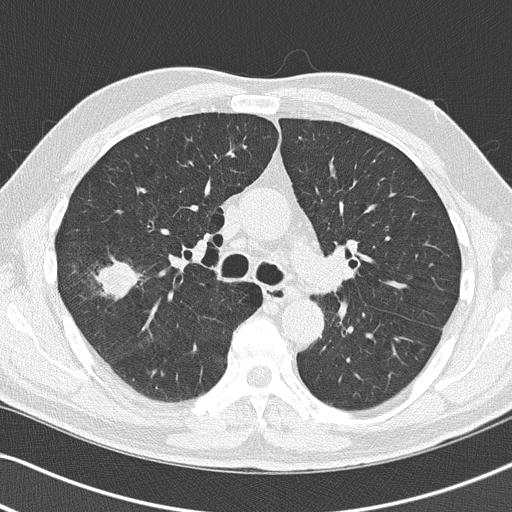
Low-dose screening chest CT, axial slice. First (baseline) screen. Lung window (W 1500 / L -600 HU). 2 mm slice thickness. Male participant, aged 67 years at enrolment.
Expert reader's lesion annotation, bounding box [x1, y1, x2, y2] px = [72, 254, 148, 318]. Screening reader's record for this exam (one nodule recorded; not confirmed to be the boxed lesion): non-calcified nodule or mass ≥4 mm, right upper lobe, 26 × 24 mm, spiculated (stellate) margins, soft tissue attenuation. Later outcome: lung cancer diagnosed 49 days after this screen — squamous cell carcinoma, NOS, right upper lobe, poorly differentiated (G3), stage IA (AJCC 6th edition), 27 mm at pathology.